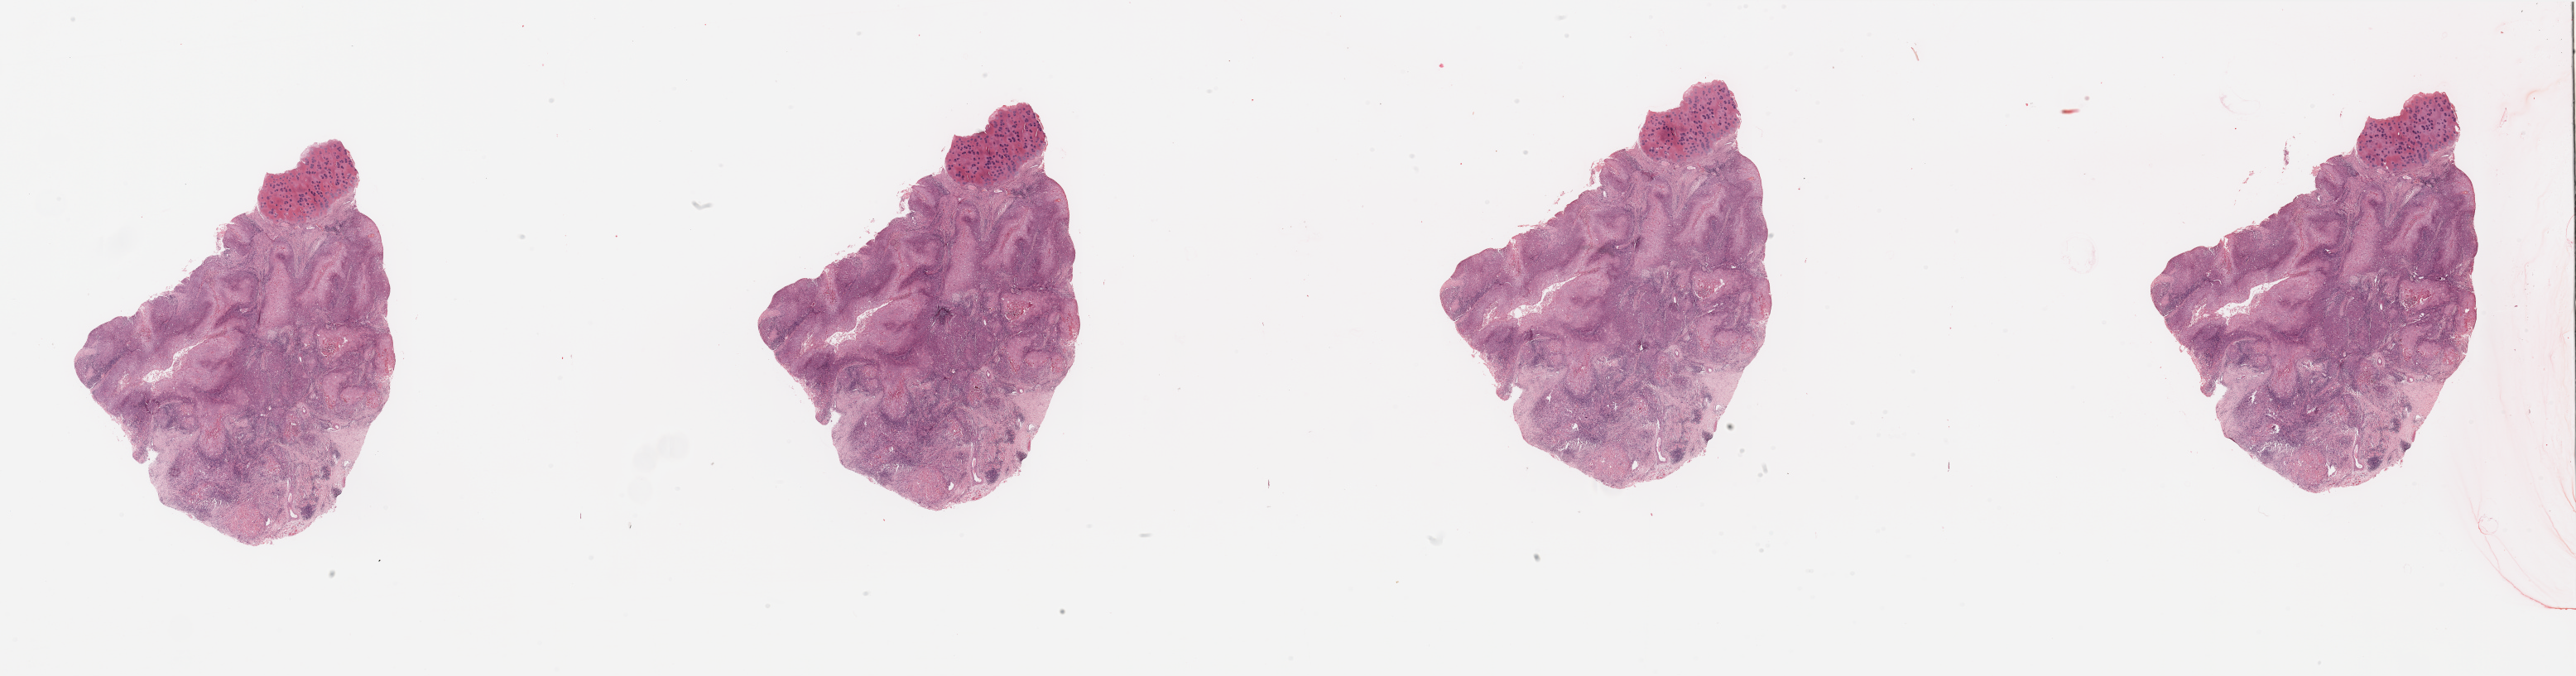
Whole-slide histology image, H&E-stained, a low-resolution overview of the entire scanned area, about 49.2 x 12.9 mm (slide scanned at 20x), head and neck, tissue type not recorded. Male, 81 y/o.
Patient diagnosis: Squamous cell carcinoma, NOS.